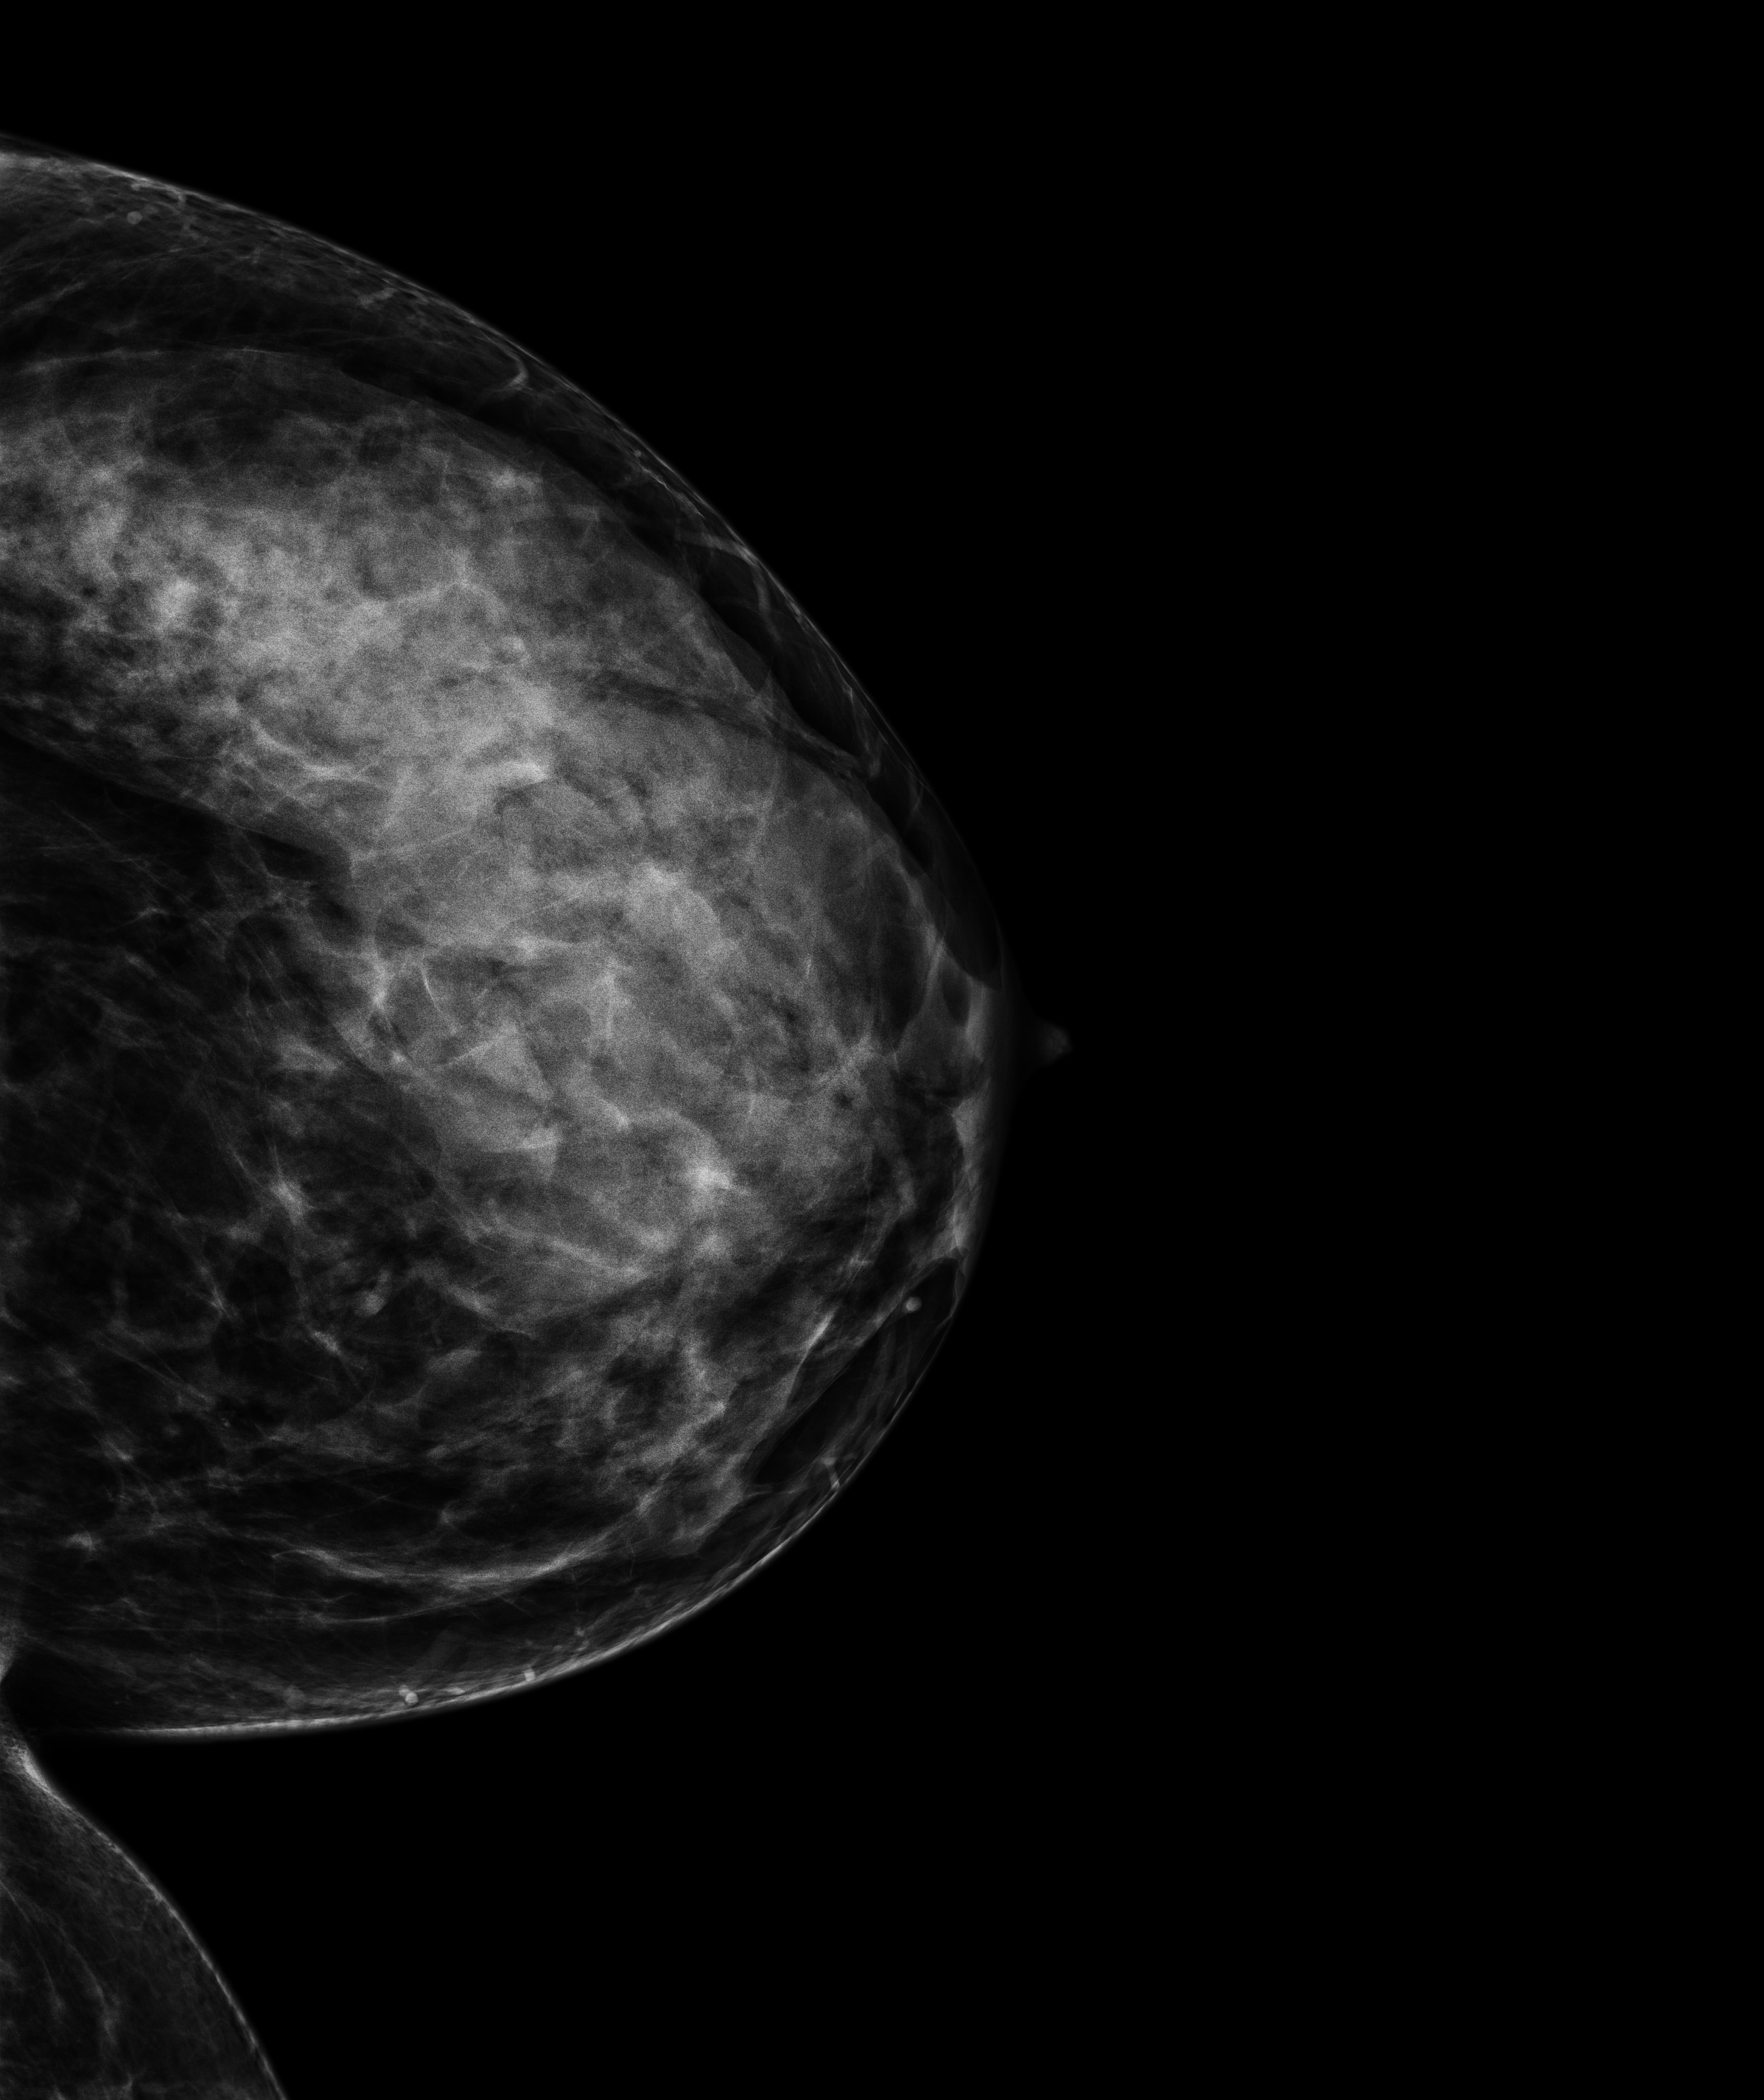
Screening examination. Patient aged 44 years (female).
Image type: full-field digital mammogram. Breast: left. Projection: CC view.